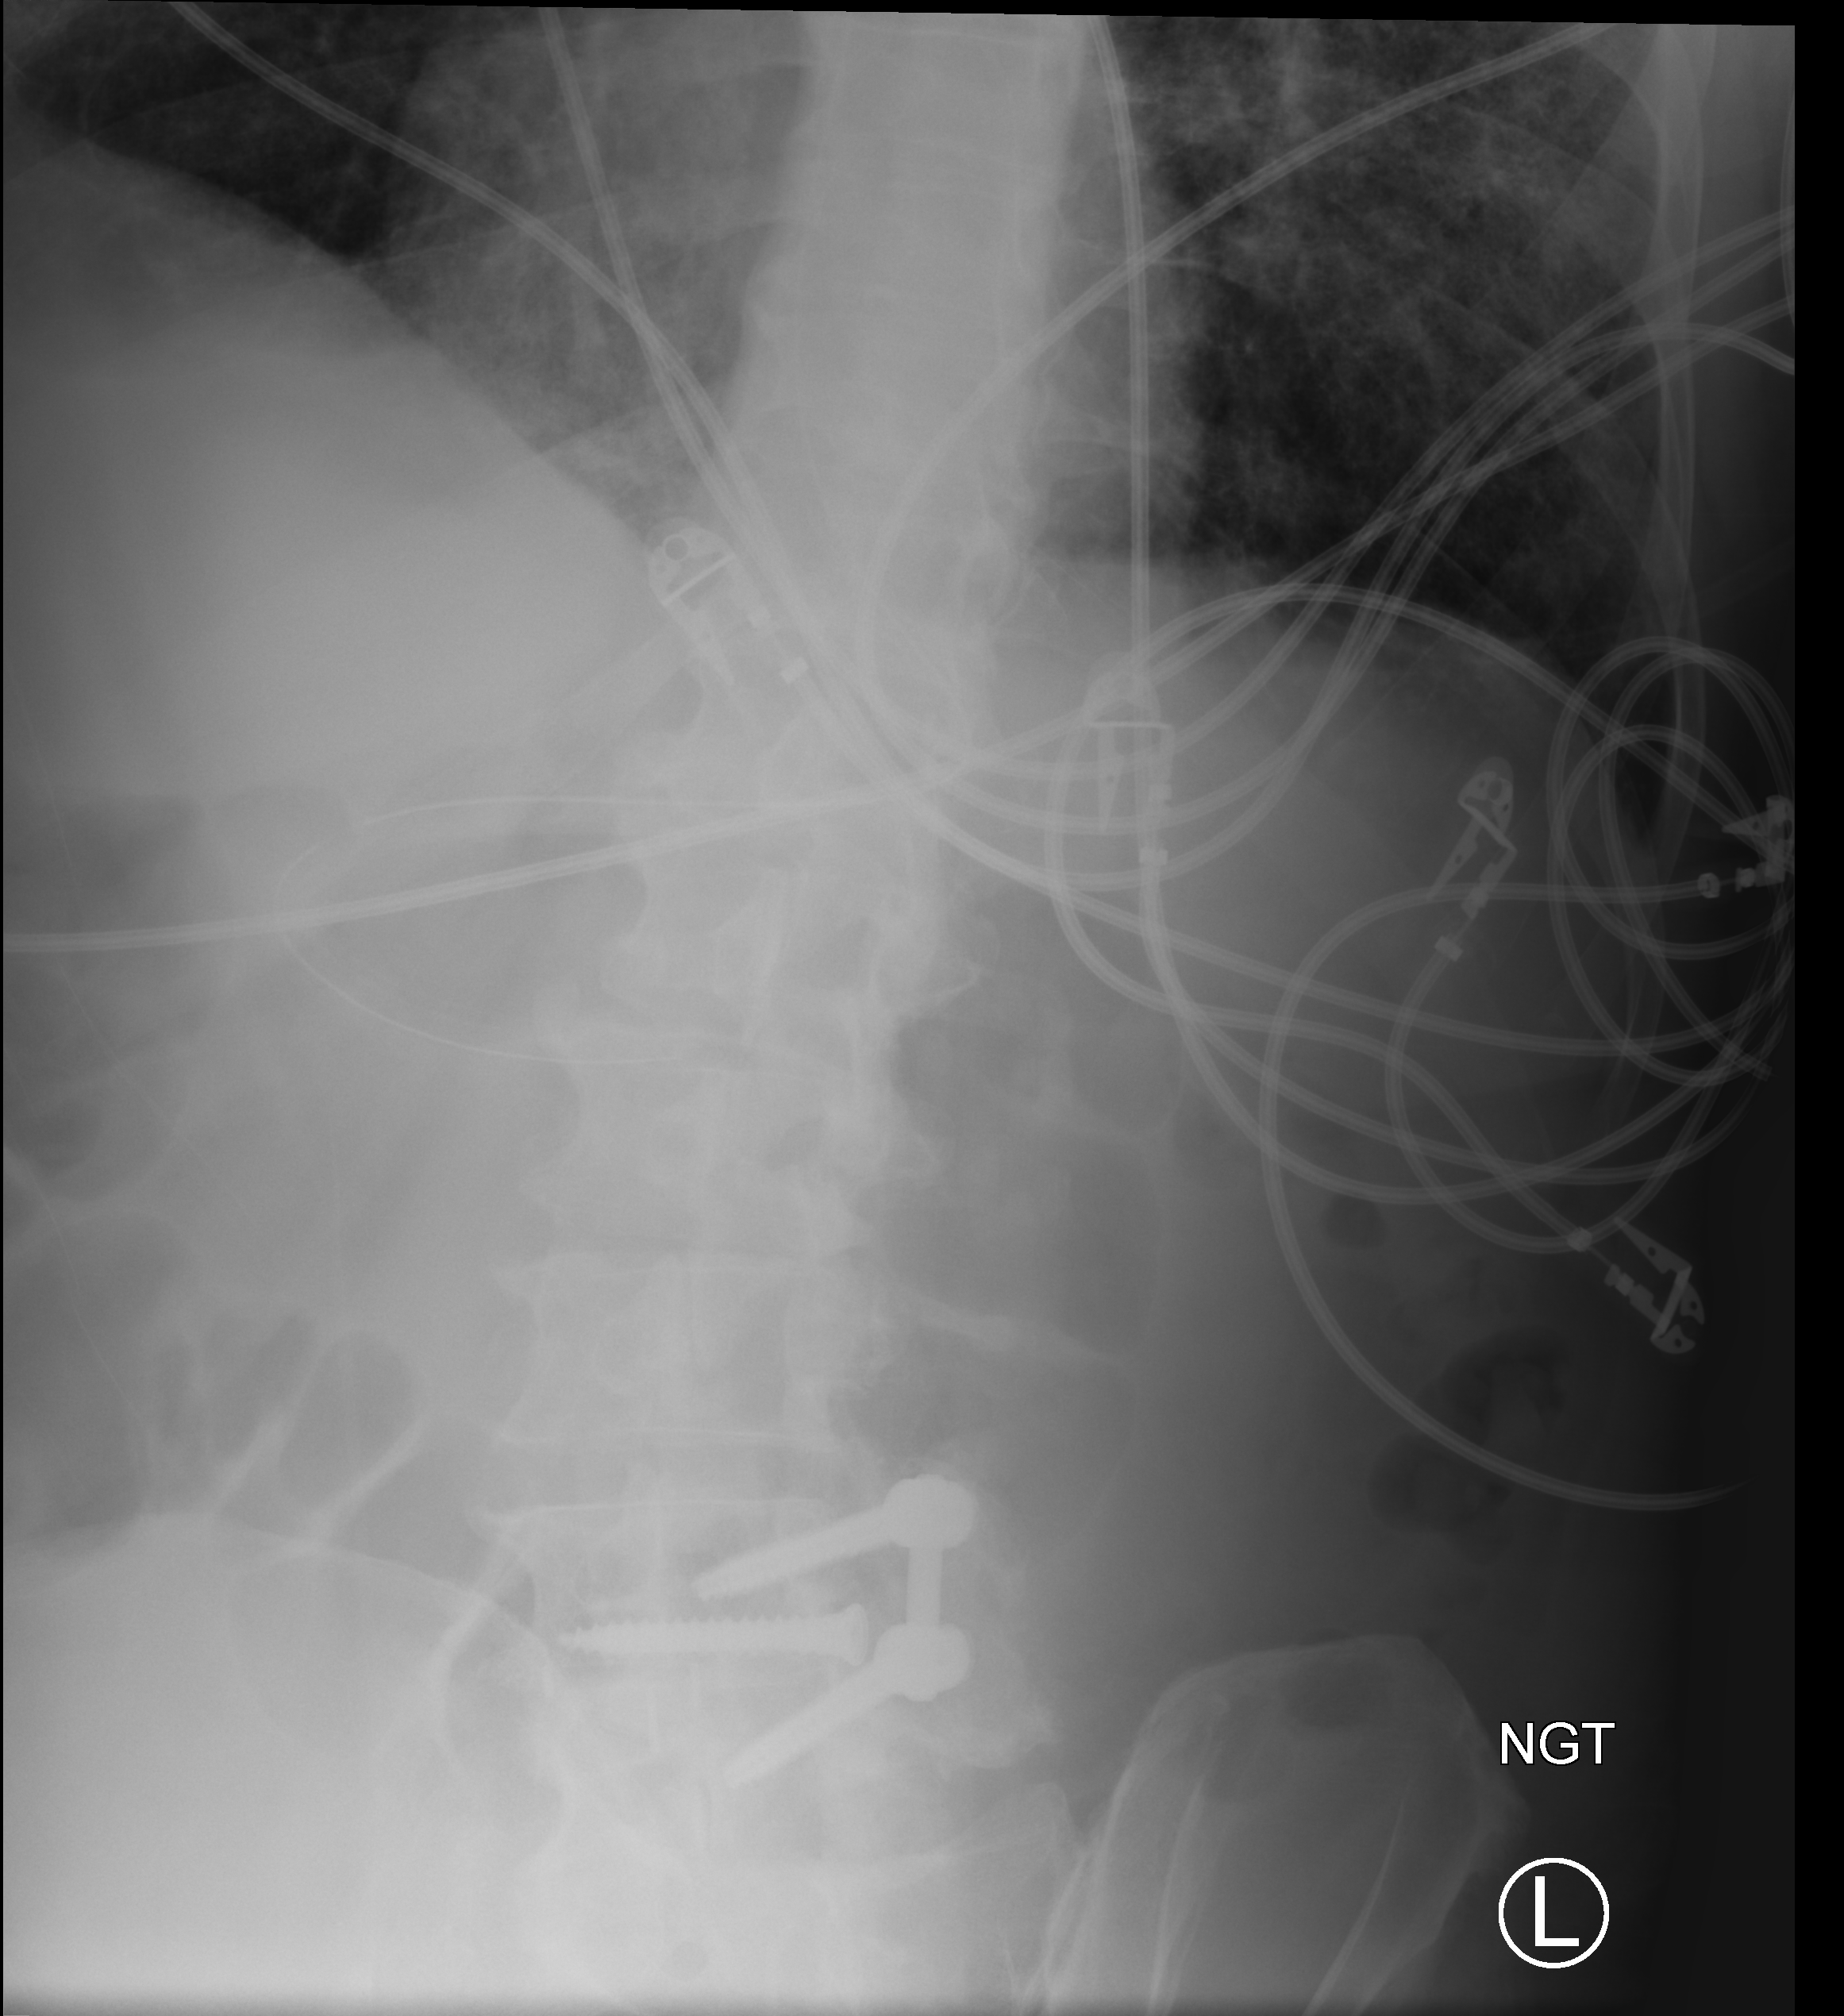
Portable abdomen radiograph. Patient hospitalised with COVID-19; male, aged 60–74 years.
Hospital-stay facts (about this admission, not read from this image; timing relative to this image not recorded):
- admitted to intensive care during this hospital stay: yes
- mechanically ventilated during this hospital stay: yes